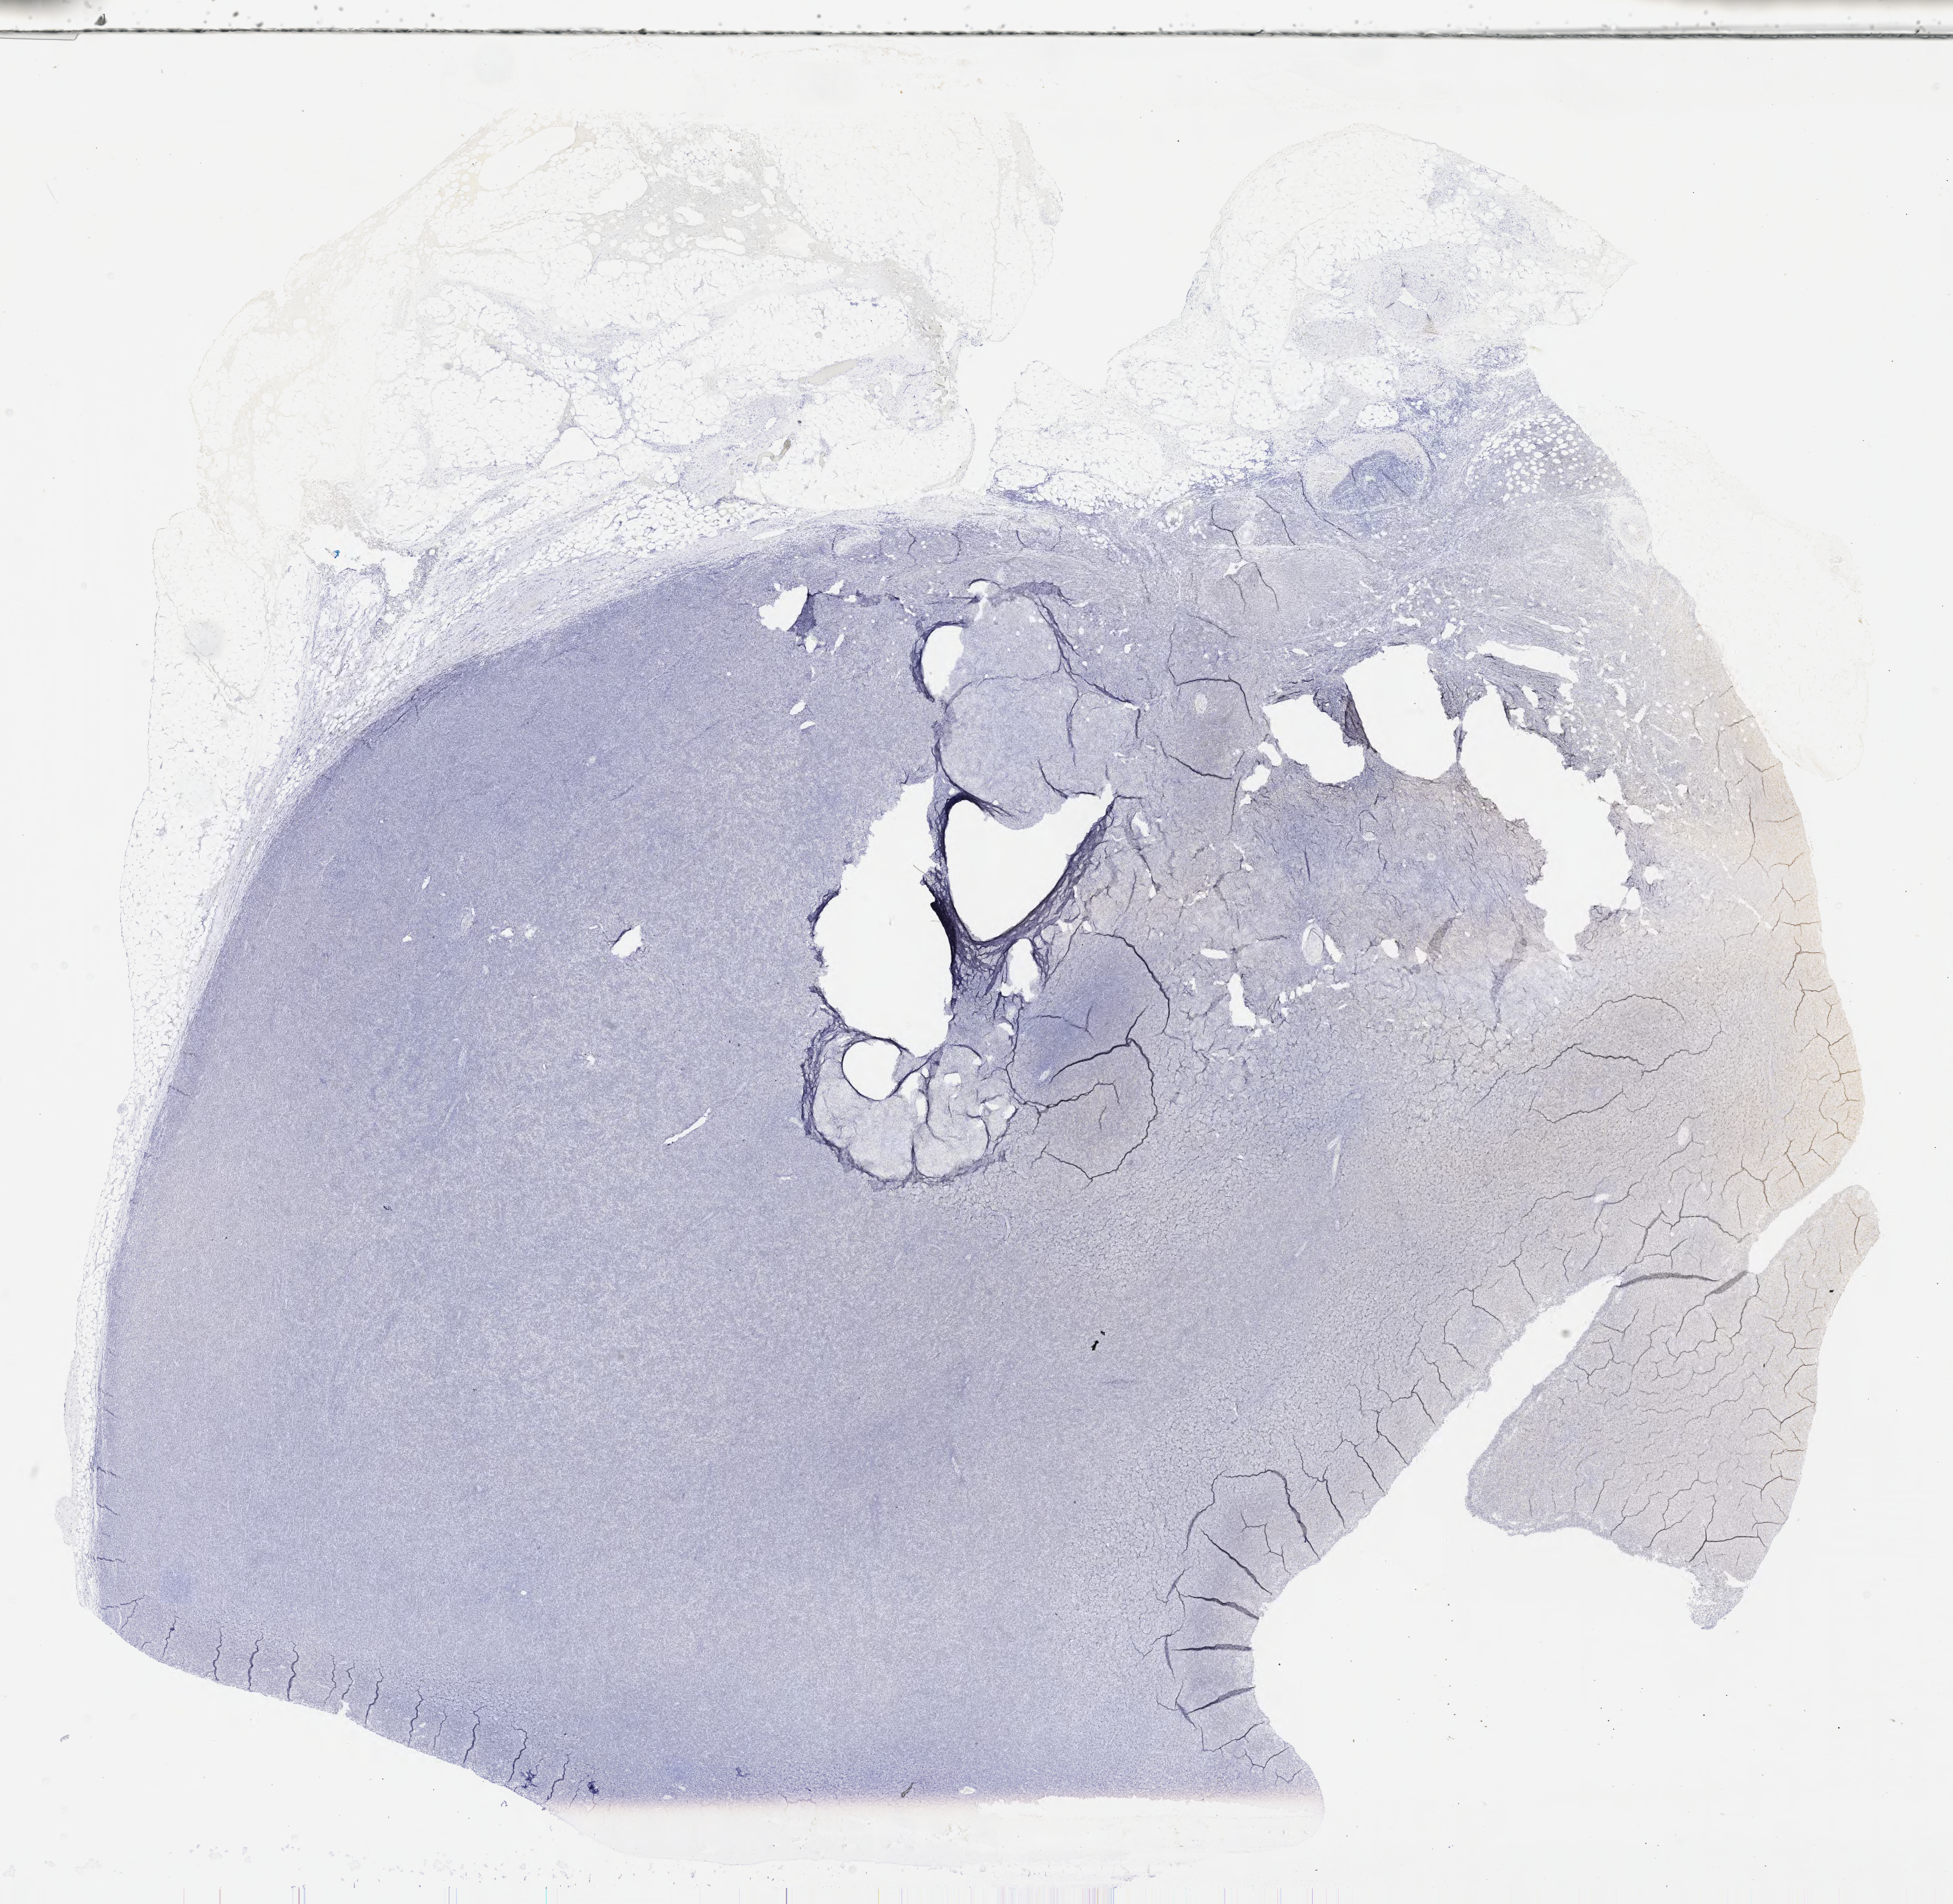
IHC for p53, whole-slide image, low-resolution overview of the scanned area, about 23.6 x 23.0 mm; tumor tissue; anatomic site: lymph node. Male patient, aged 54.
Histologic diagnosis: Diffuse large B-cell lymphoma, NOS.